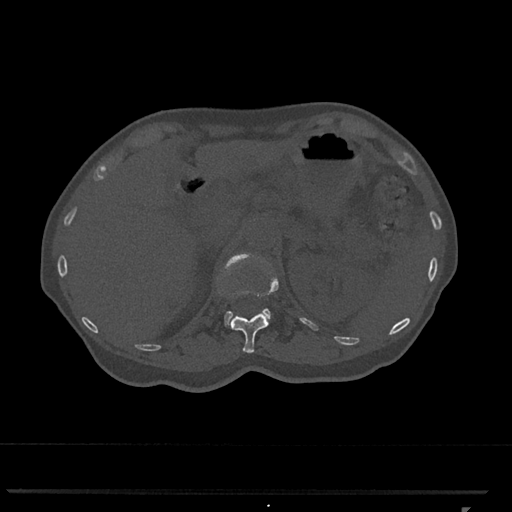
CT including the spine, one axial slice. Slice 441 of 793 in the series (ordered by position). 120 kVp. Bone window (W 1800 / L 400 HU). 0.5 mm slice thickness. 512 × 512 image matrix, field of view 380 × 380 mm. Patient: female, 62 years. Case-level facts recorded for this patient, not image findings: primary cancer: renal.
Outlined on this slice (semi-automatically segmented with operator editing):
- L1 vertebra: bounding box [x1, y1, x2, y2] px = [224, 253, 271, 326]
- T12 vertebra: [228, 254, 279, 353]